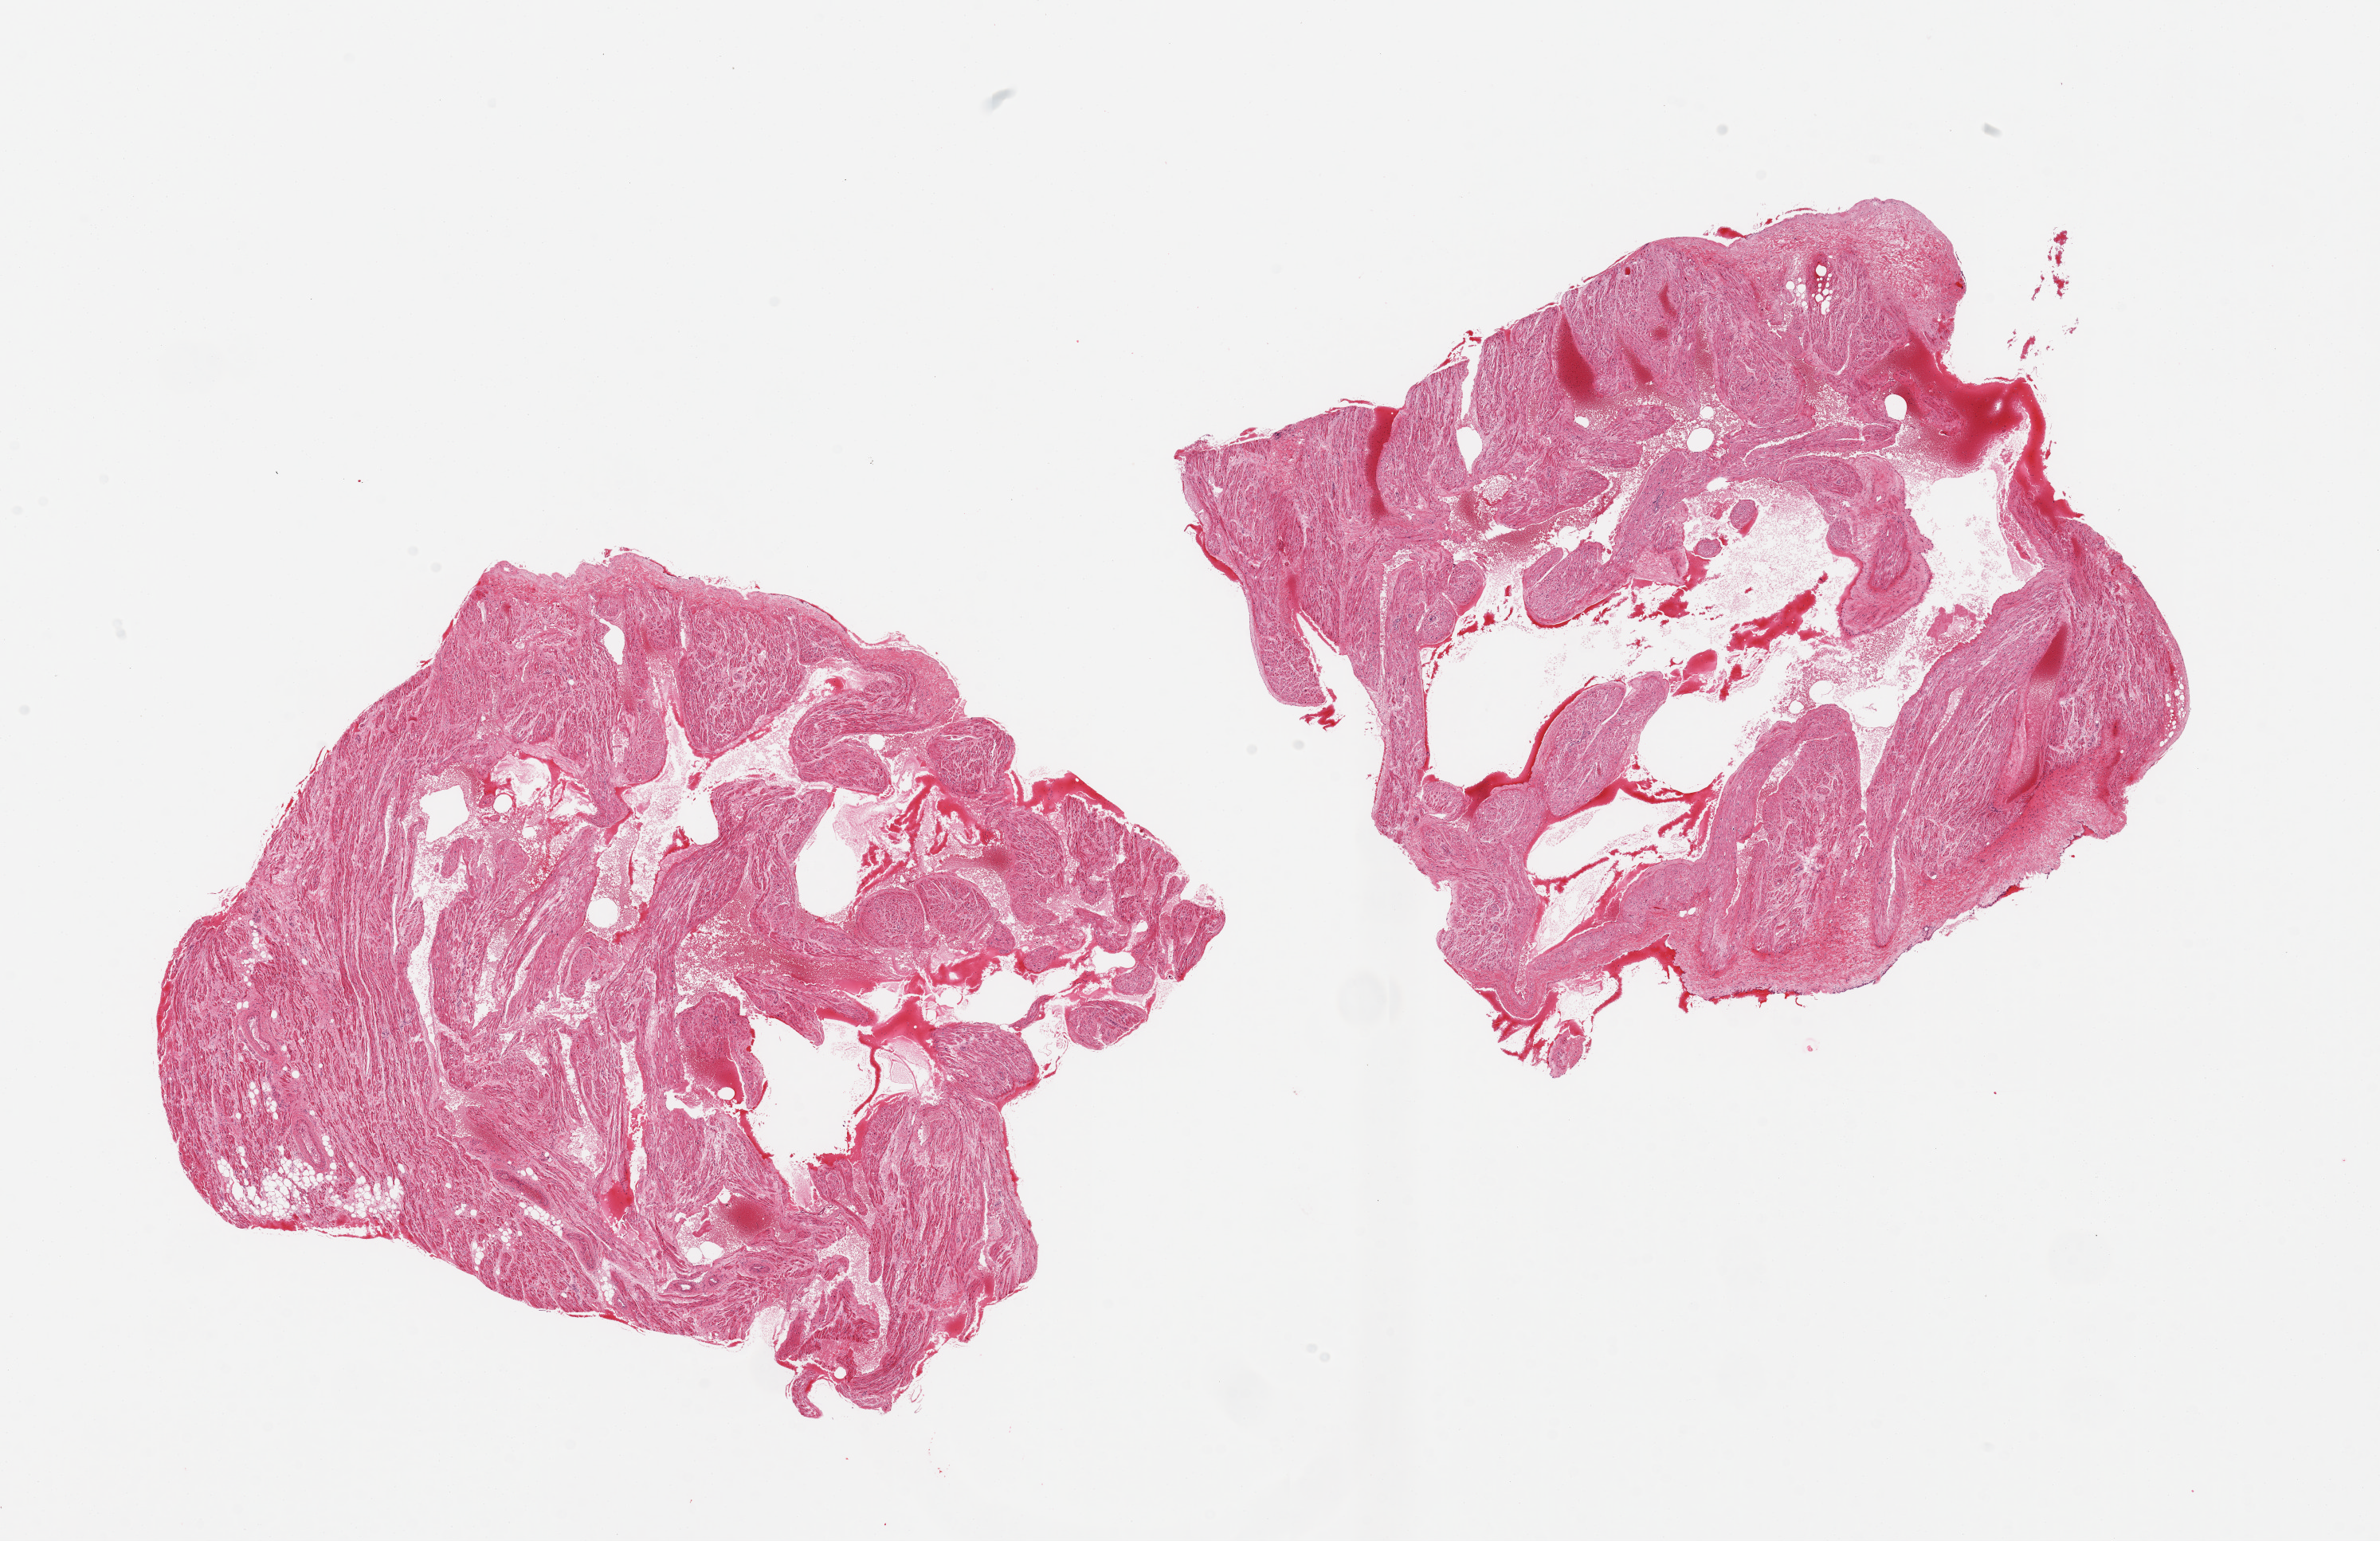
Haematoxylin and eosin whole-slide image, brightfield, shown as a low-resolution overview of the whole scanned area (about 23.6 x 15.3 mm, slide scanned at 20x), PAXgene-fixed, paraffin-embedded tissue, section of auricular appendage (target tissue), donor tissue sample. Donor sex: male.
Pathologist's review note for this sample: 2 pieces, no abnormalities.